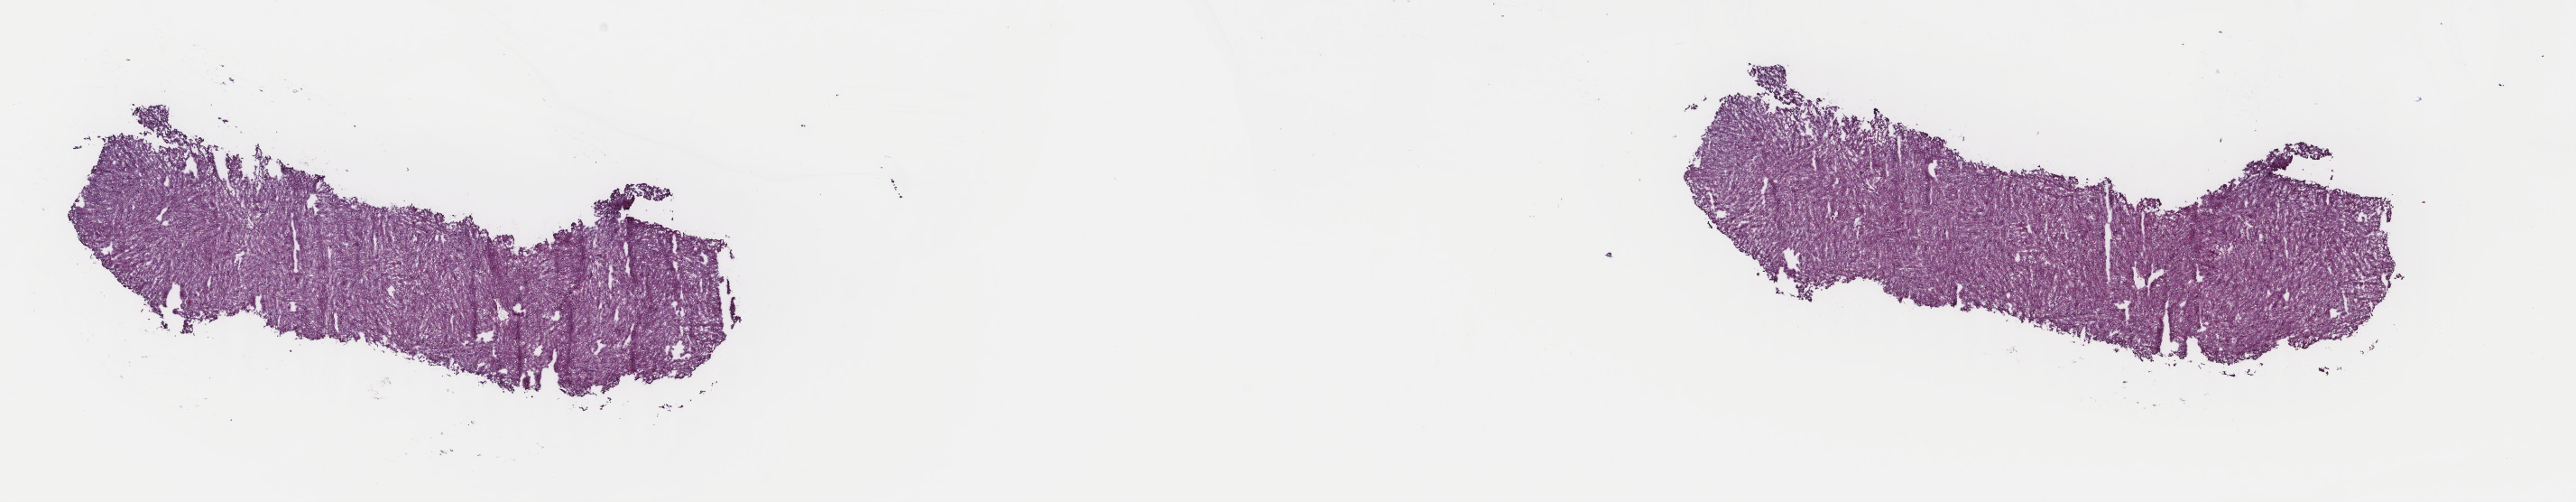
Hematoxylin and eosin (H&E) stained whole-slide image, low-resolution overview of the scanned area, about 22.7 x 4.4 mm (acquisition: 40x scan); frozen section from the top of the tissue portion; primary tumour sample from the adrenal cortex. Male patient; age at initial diagnosis 55 years.
Histologic diagnosis: Adrenal cortical carcinoma (cortex of adrenal gland).